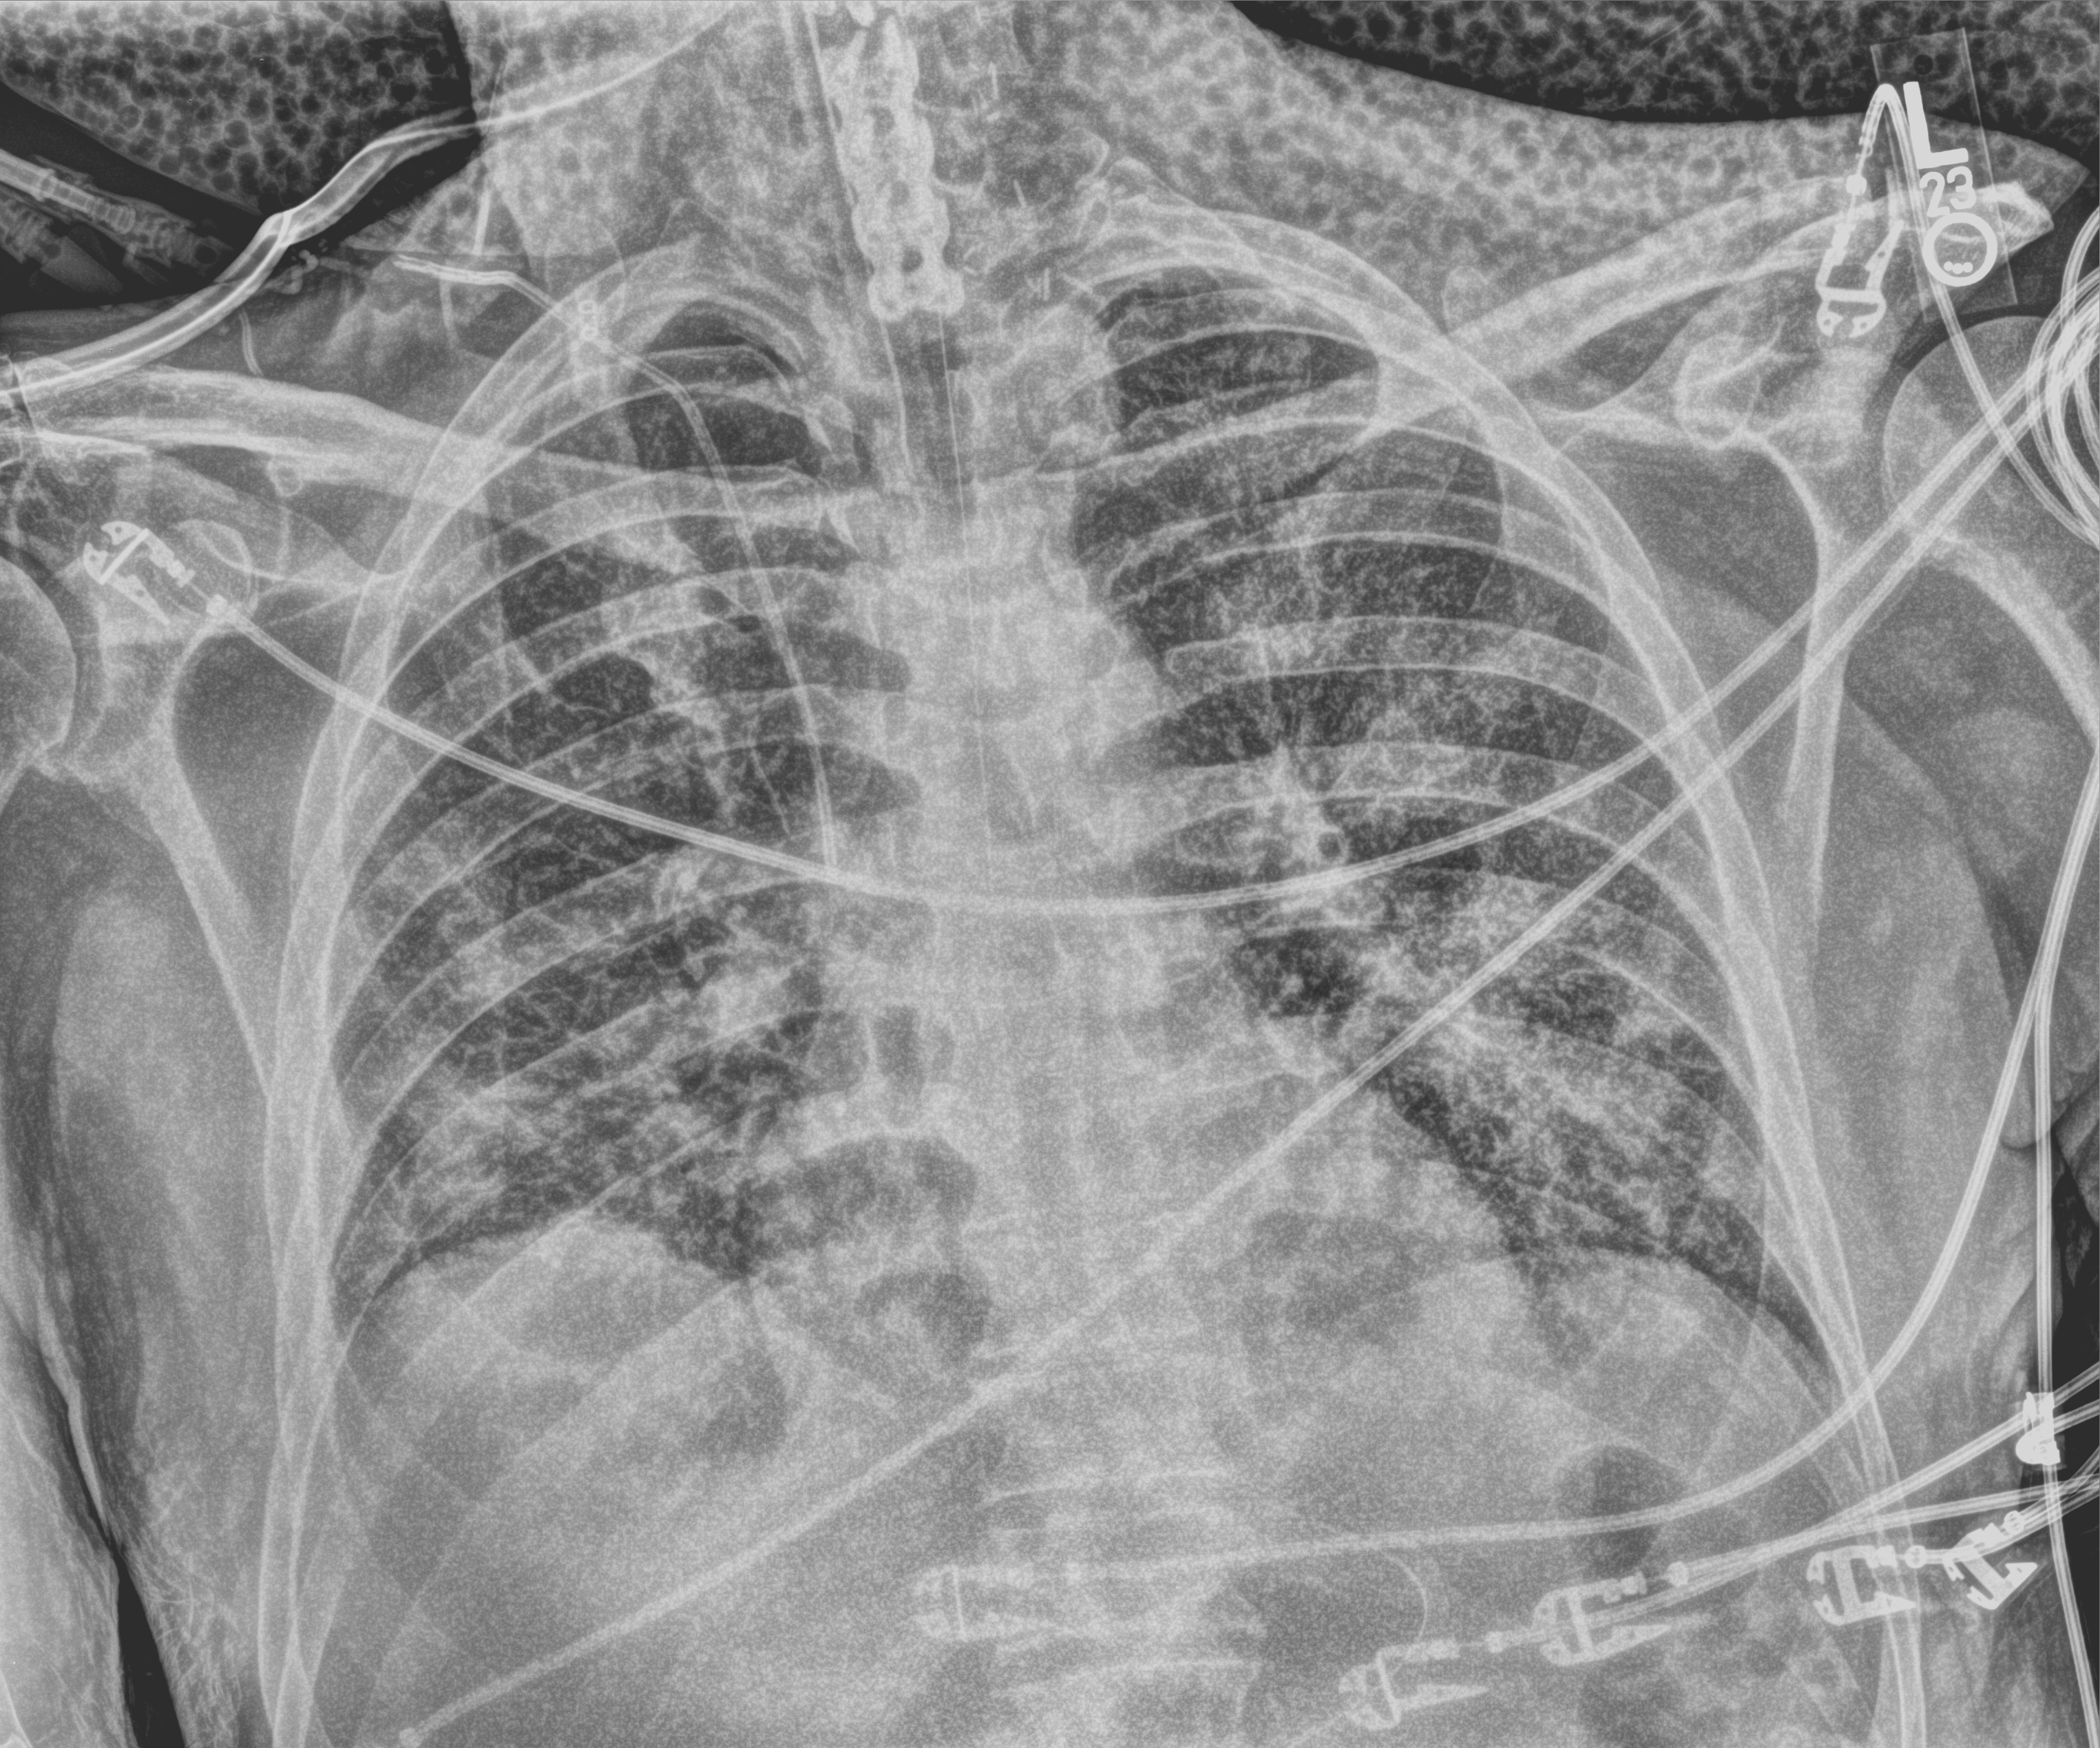
Bedside chest radiograph (computed radiography), anteroposterior (AP) projection. Patient hospitalised with COVID-19; male, aged 60–74 years.
From the hospital-stay record, not from the radiograph (when in the stay this image was taken is not recorded):
- admitted to intensive care during this hospital stay: yes
- mechanically ventilated during this hospital stay: yes
- length of hospital stay: 43 days